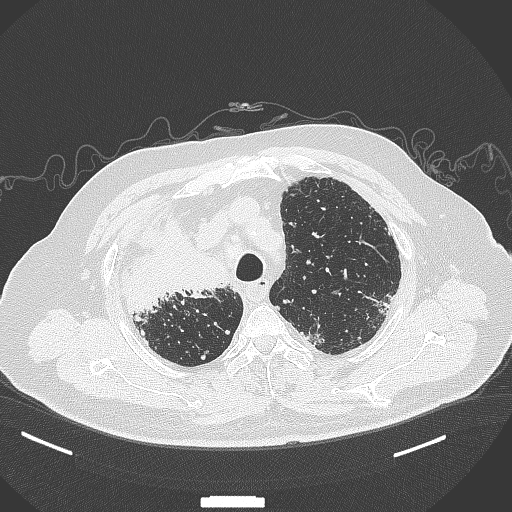
Chest CT, one axial slice. Slice 287 of 384 in the series (ordered by position). 120 kVp. Lung window (W 1500 / L -600 HU). 1 mm slice thickness. 512 × 512 image matrix, field of view 400 × 400 mm. Male patient, age 69 years. From the clinical record (not read from this slice): clinical TNM (as recorded): T4 N3 M1.
Outlined on this slice (bounding box drawn by a radiologist):
- lung tumour (recorded histology: adenocarcinoma): box from (x=123, y=215) to (x=235, y=311) px